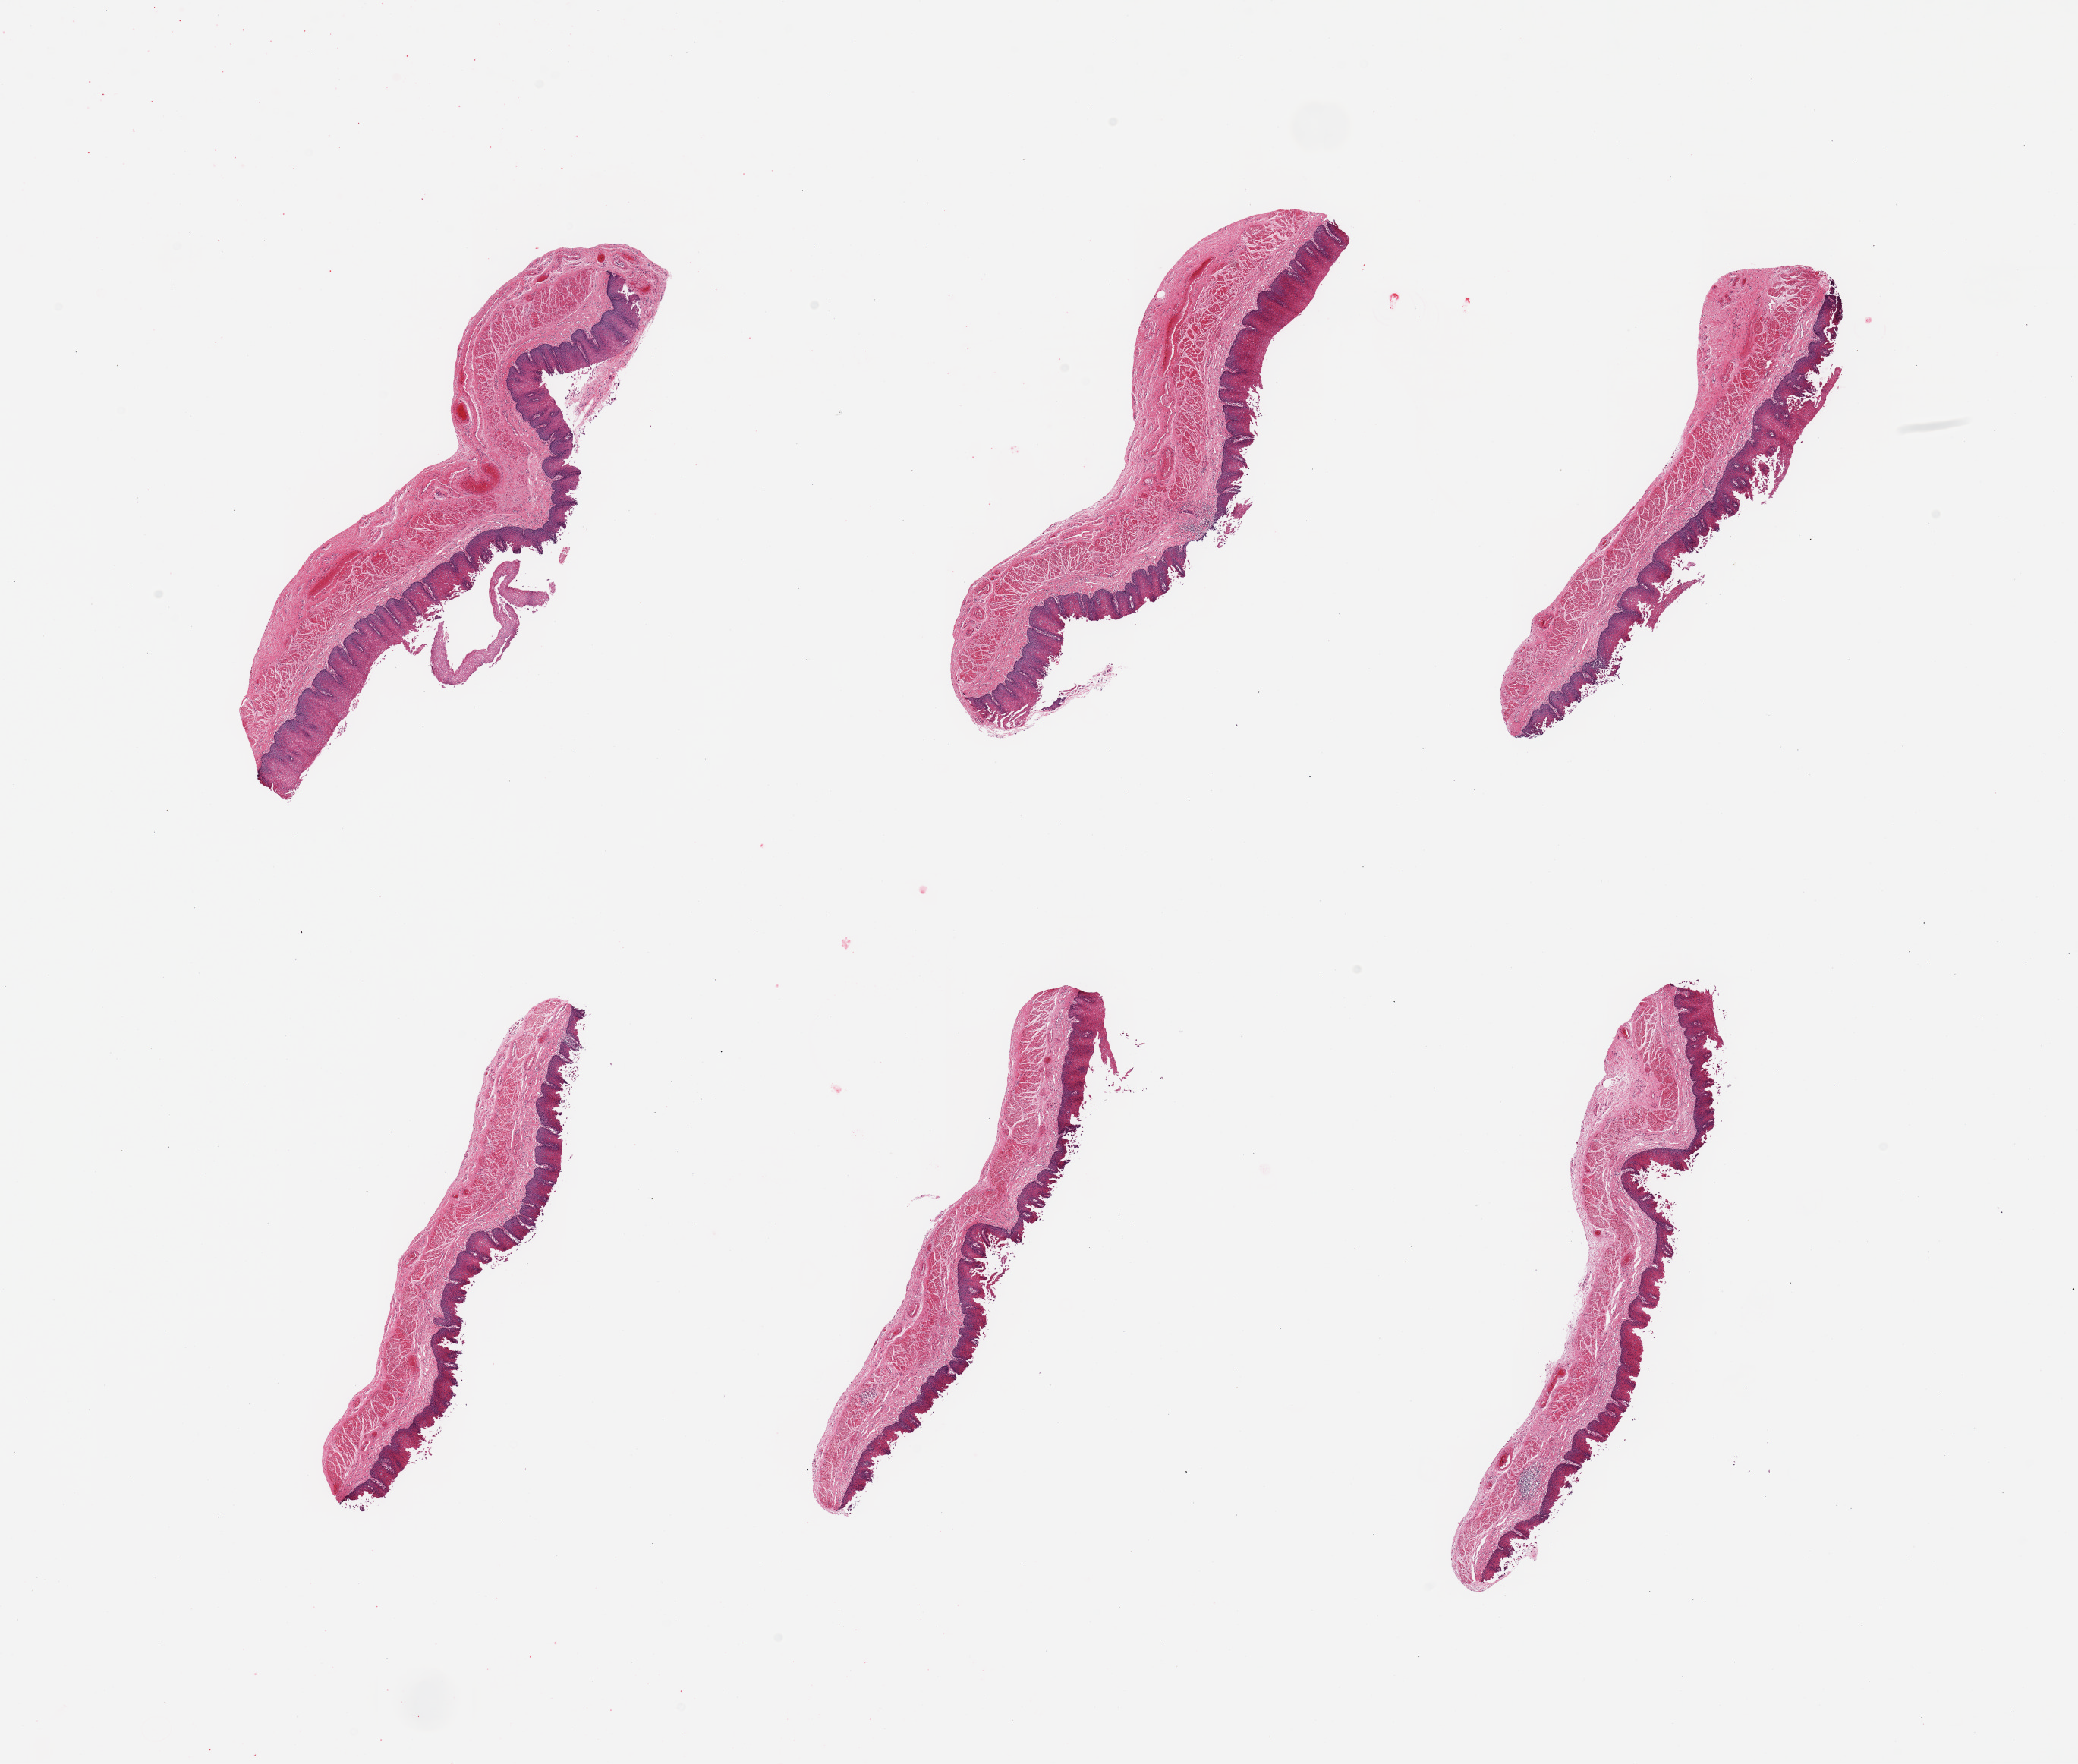
Digitized hematoxylin and eosin (H&E)-stained section, whole scanned area (about 21.7 x 18.4 mm) shown as a low-resolution overview, PAXgene-fixed paraffin-embedded (PFPE) section, section of esophageal mucous membrane (target tissue), tissue donor sample. Female donor.
Review note (as recorded): 6 pieces; moderate sloughing of squamous epithelium; well dissected.